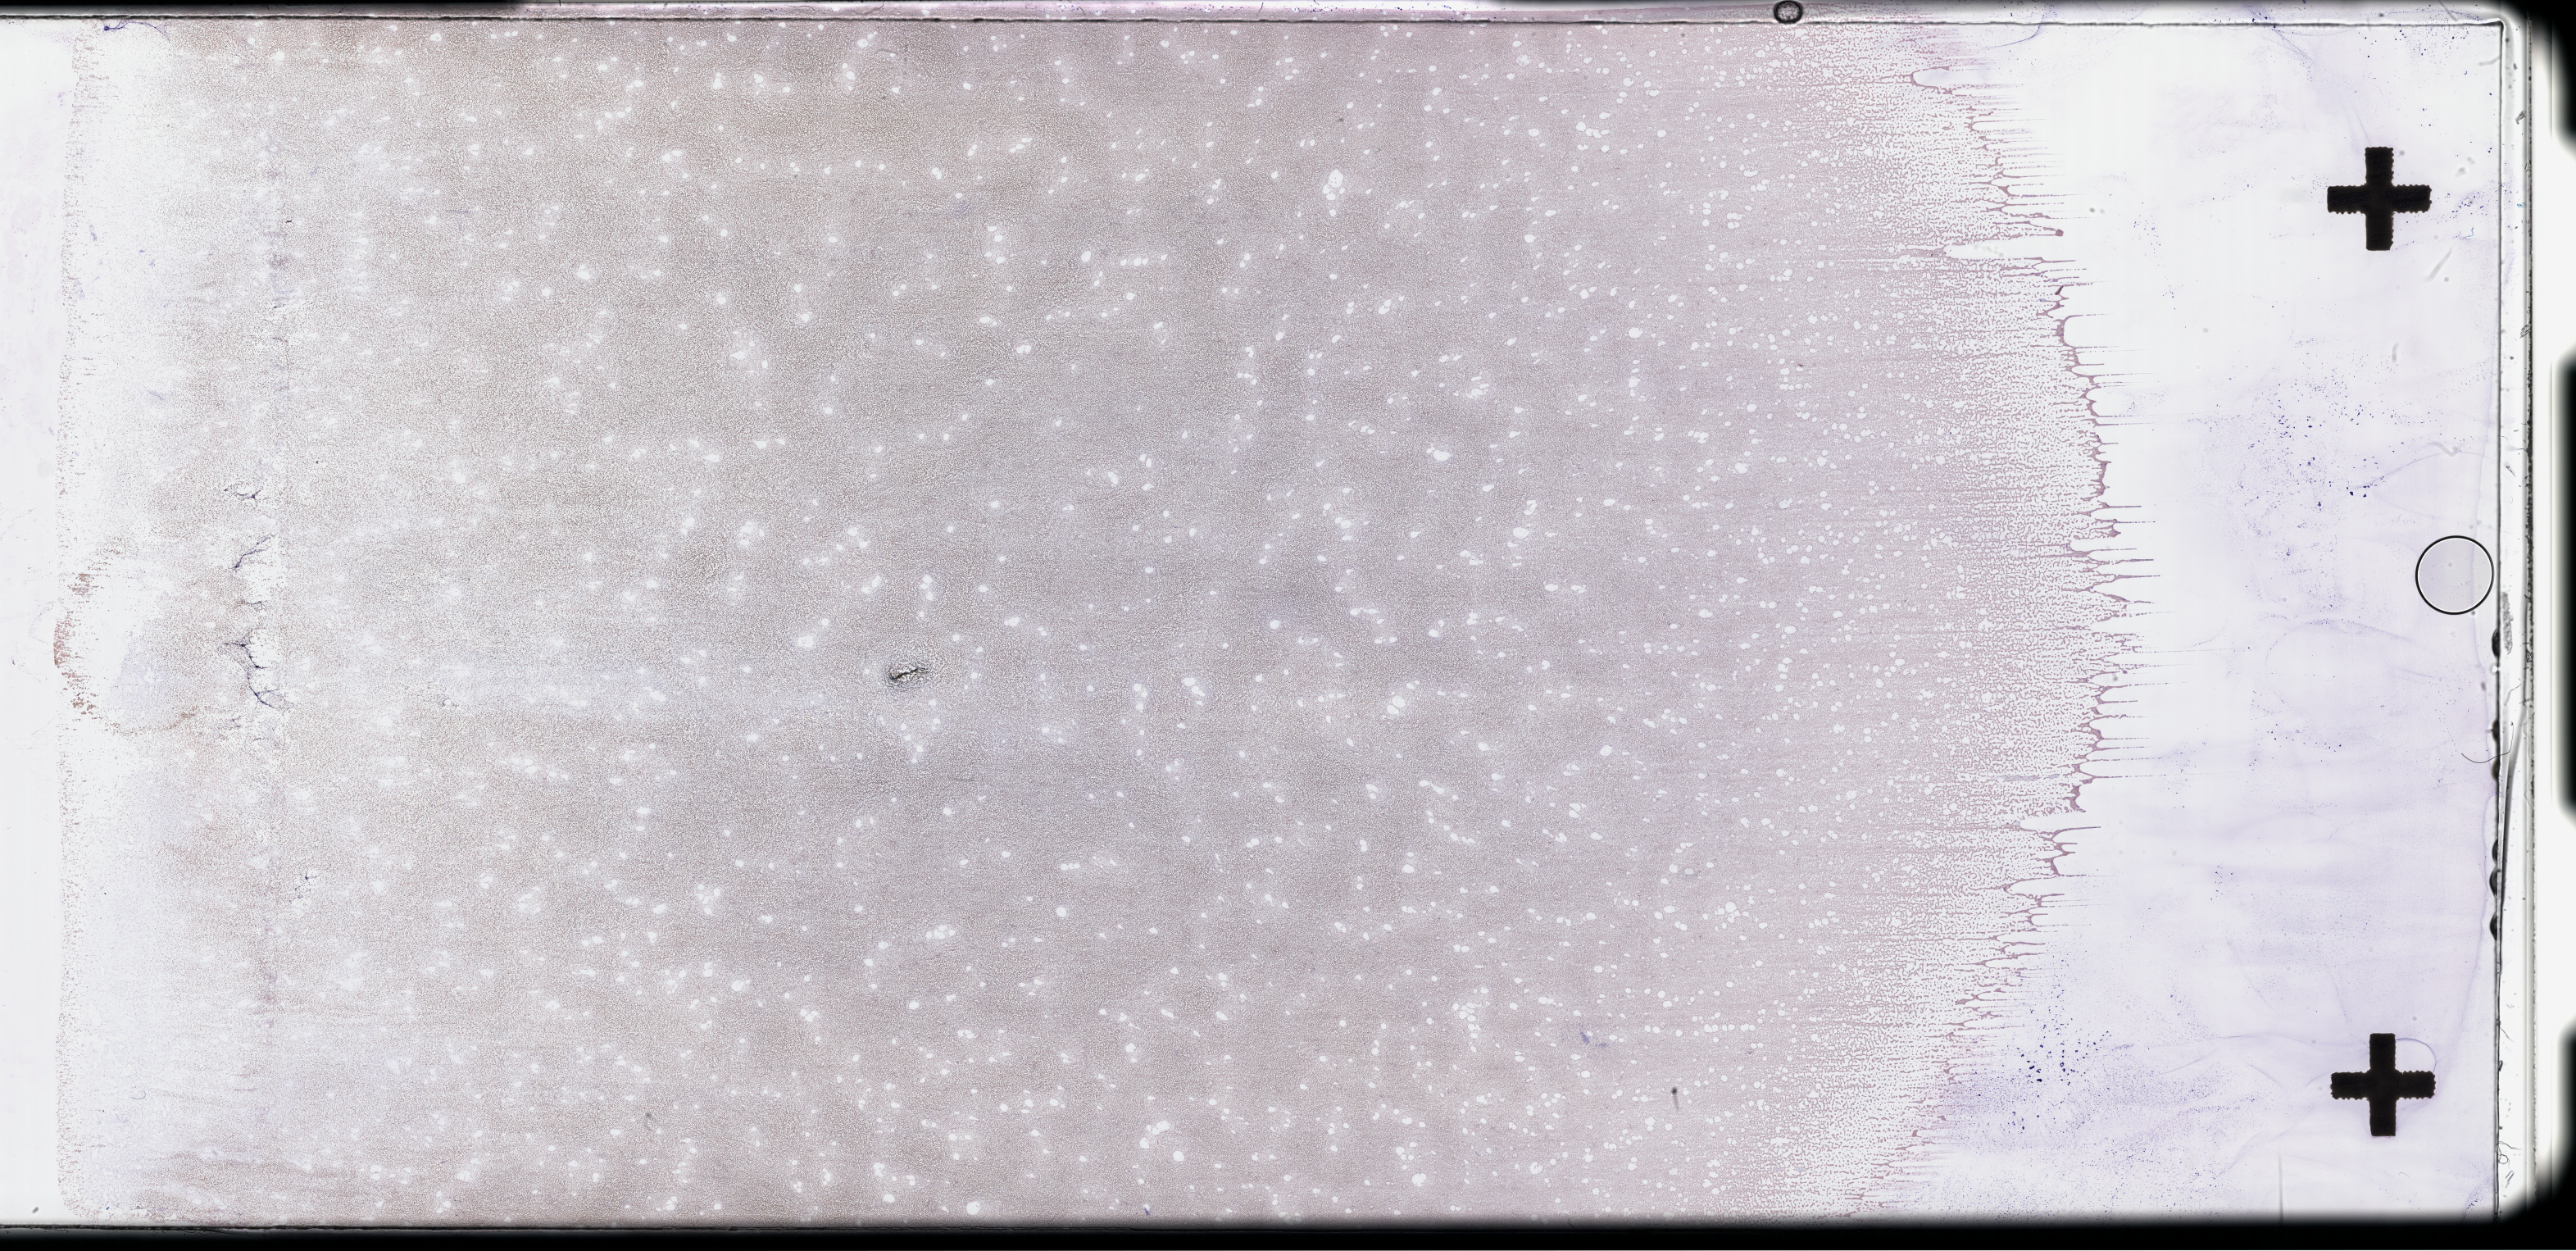
Wright-Giemsa-stained whole blood smear, whole-slide image — low-resolution overview of the scanned area, about 50.8 x 24.6 mm. Collected at disease progression. Patient: female.
From a patient with: Acute Myeloid Leukemia Not Otherwise Specified.